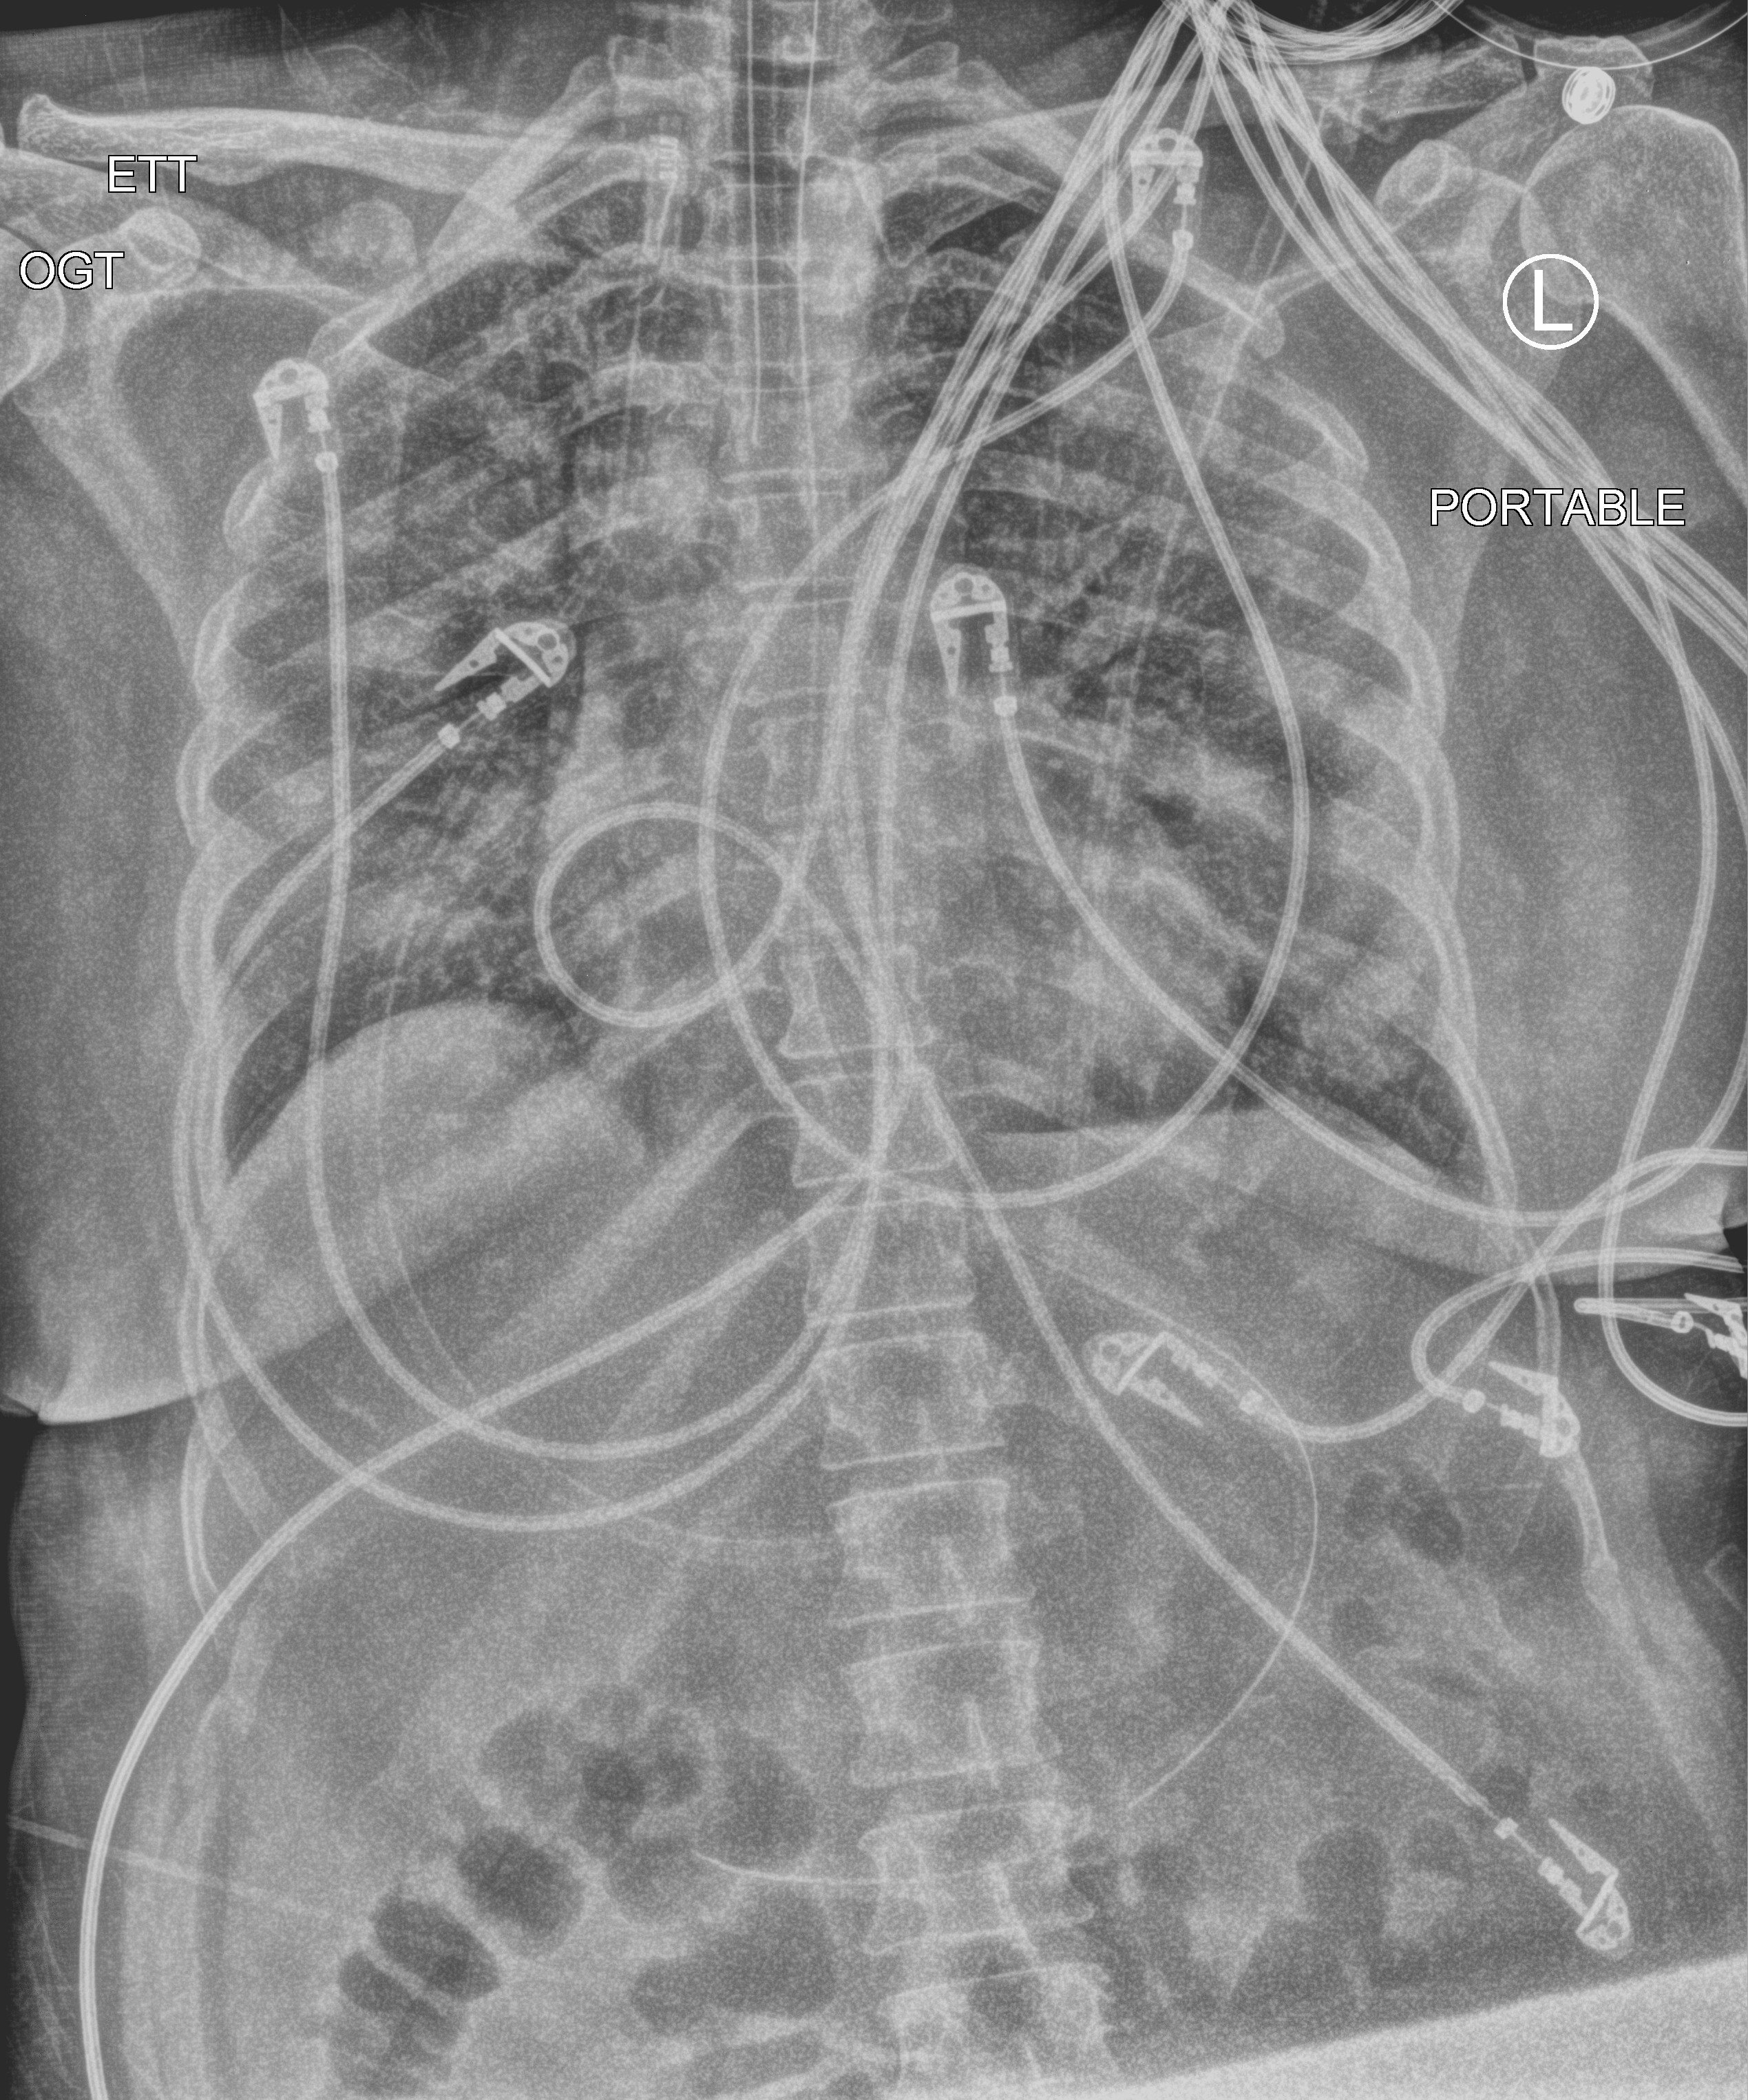
Chest X-ray (portable); anteroposterior (AP) projection. Patient hospitalised with COVID-19; male, aged 18–59 years.
From the hospital-stay record, not from the radiograph (when in the stay this image was taken is not recorded):
- admitted to intensive care during this hospital stay: yes